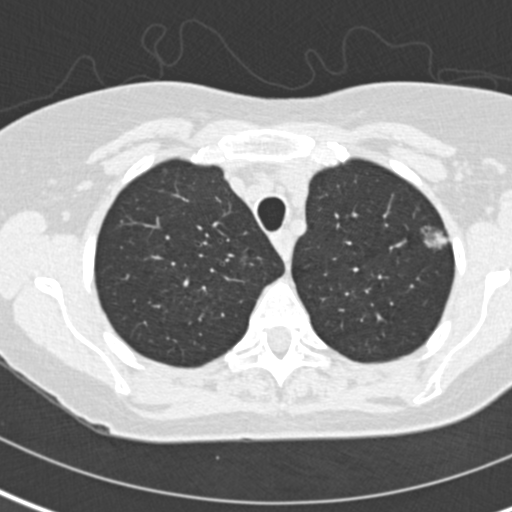
Chest CT (low-dose screening protocol), one axial image. Second annual screen. Lung window (W 1500 / L -600 HU). Standard (soft-tissue) reconstruction kernel (B30f). 512 × 512 image matrix. Female participant, aged 60 years at enrolment.
Lesion marked by an expert reader, bounding box (x1, y1, x2, y2) in pixels: (415, 224, 464, 264). The screening reader recorded 2 non-calcified nodules or masses ≥4 mm on this exam; which of them this box marks is not recorded. Official screen result: positive, change unspecified: nodule(s) >= 4 mm or enlarging nodule(s), mass(es), or other non-specific abnormalities suspicious for lung cancer. Later outcome: lung cancer diagnosed 116 days after this screen — adenocarcinoma, NOS, left upper lobe, moderately differentiated (G2), stage IA (AJCC 6th edition), 11 mm at pathology.